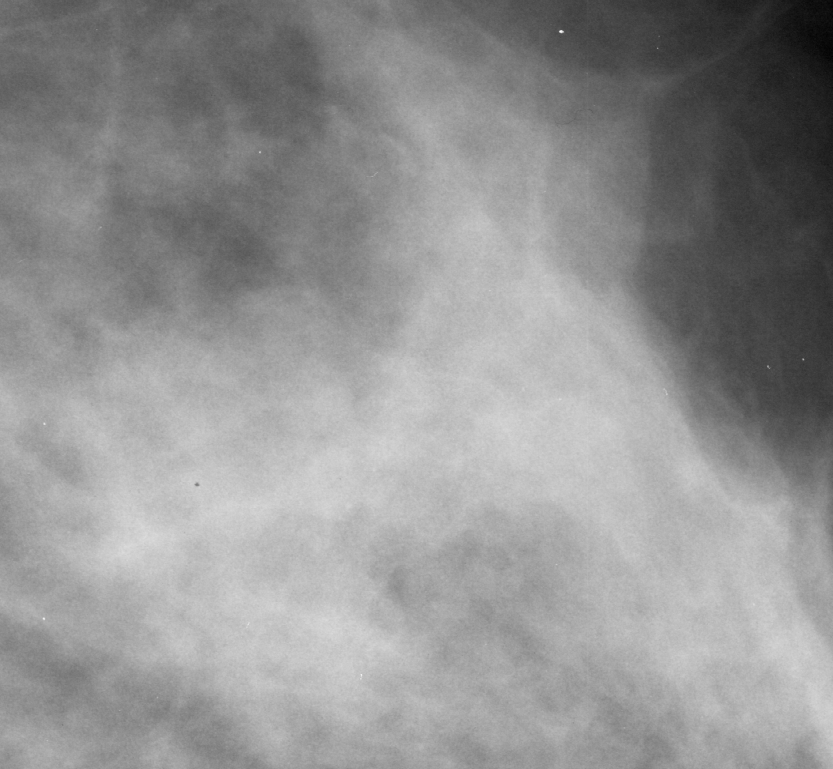
Crop from a digitized film mammogram around one marked abnormality; left breast; MLO view; BI-RADS breast density category 3 (scale 1–4).
- Marked abnormality: calcifications, morphology punctate / pleomorphic, distribution clustered; BI-RADS assessment category 4; subtlety rating 2 on a 1 (subtle) to 5 (obvious) scale; pathology (as recorded): benign.